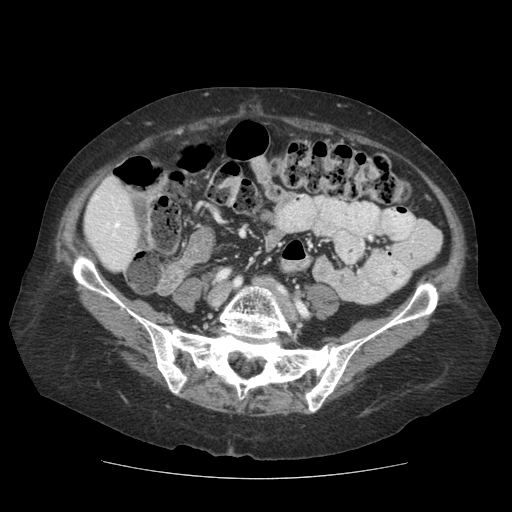
Contrast-enhanced abdominal CT (liver protocol), one axial slice; reconstruction kernel STANDARD; soft-tissue window (W 400 / L 40 HU); 2.5 mm slice thickness; 512 × 512 image matrix. Case-level facts recorded for this patient, not image findings: diagnosis: hepatocellular carcinoma (patient treated with transarterial chemoembolisation; whether this scan precedes or follows treatment is not stated here); TNM stage (as recorded): Stage-I; Child-Pugh class: A.
Structures marked on this image (semi-automatic segmentation, software-assisted and operator-edited):
- liver parenchyma outside the tumour (the mass and vessels are separate outlines, so this box may not span the whole liver): bounding box (x1, y1, x2, y2) in pixels: (84, 177, 138, 270)
- liver vessels: (96, 197, 120, 236)